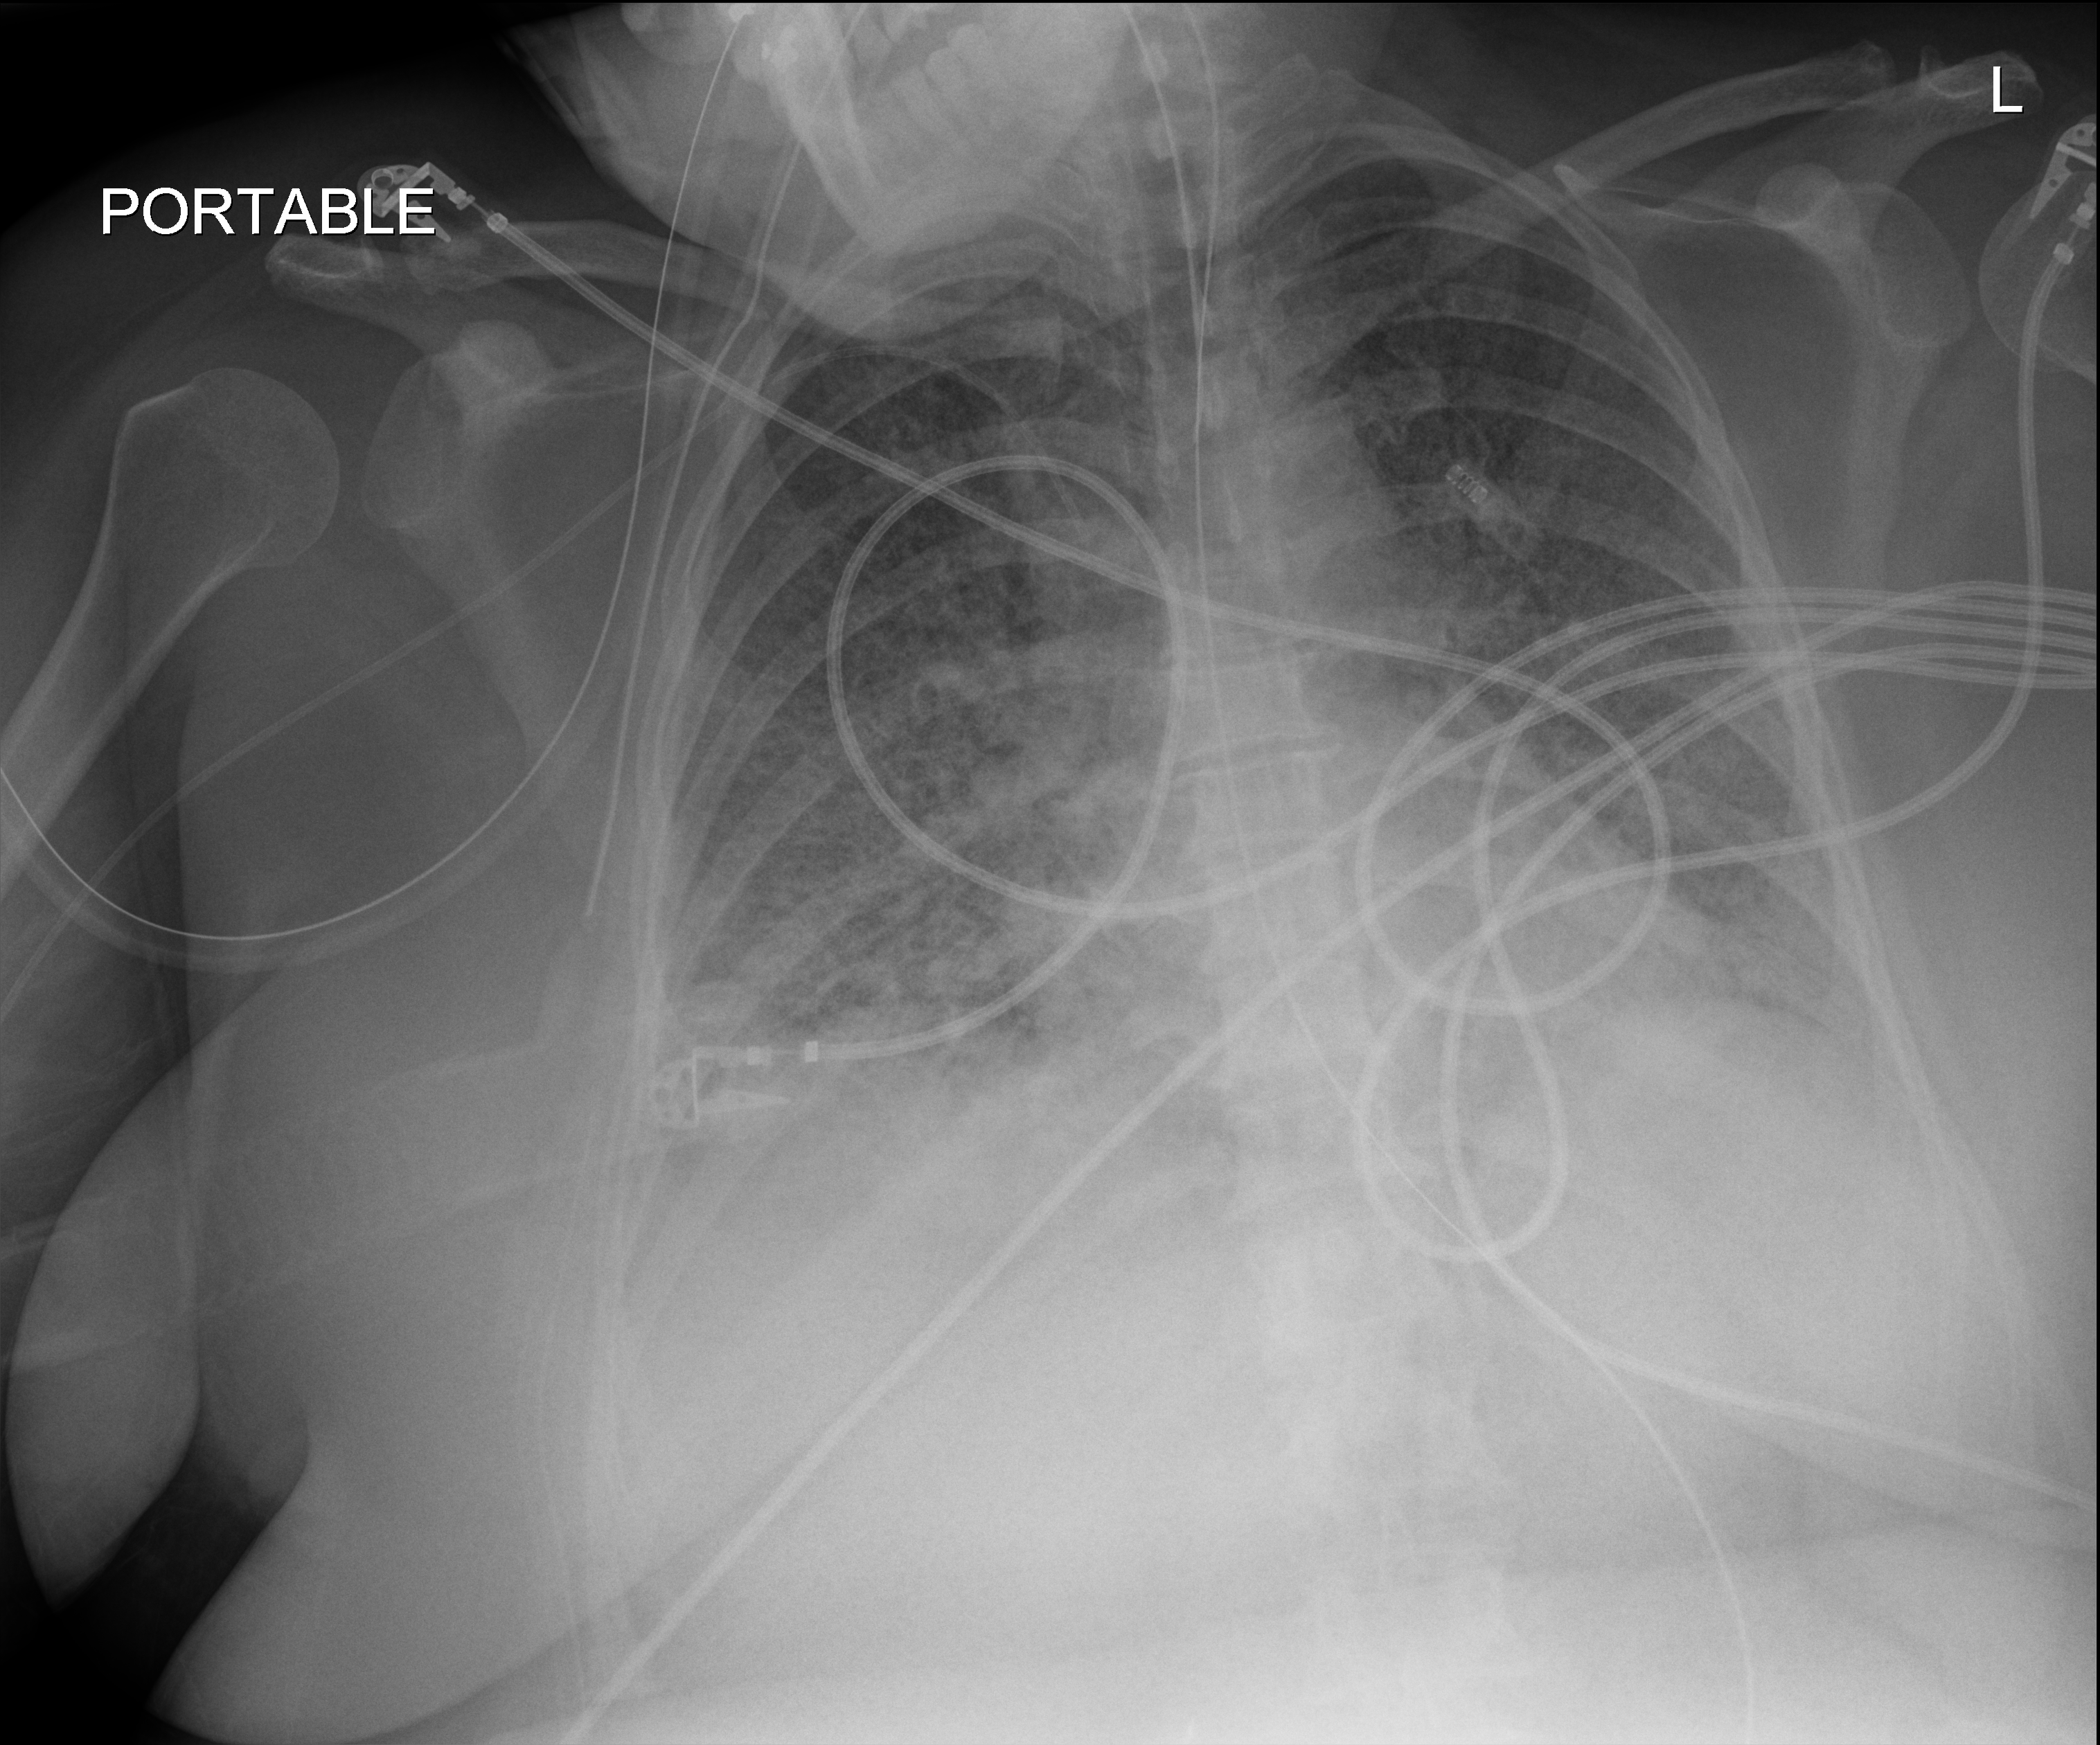
Chest X-ray (portable); anteroposterior (AP) projection. Patient hospitalised with COVID-19; female, aged 18–59 years.
From the hospital-stay record, not from the radiograph (when in the stay this image was taken is not recorded):
- mechanically ventilated during this hospital stay: yes
- length of hospital stay: 95 days
- admitted to intensive care during this hospital stay: yes